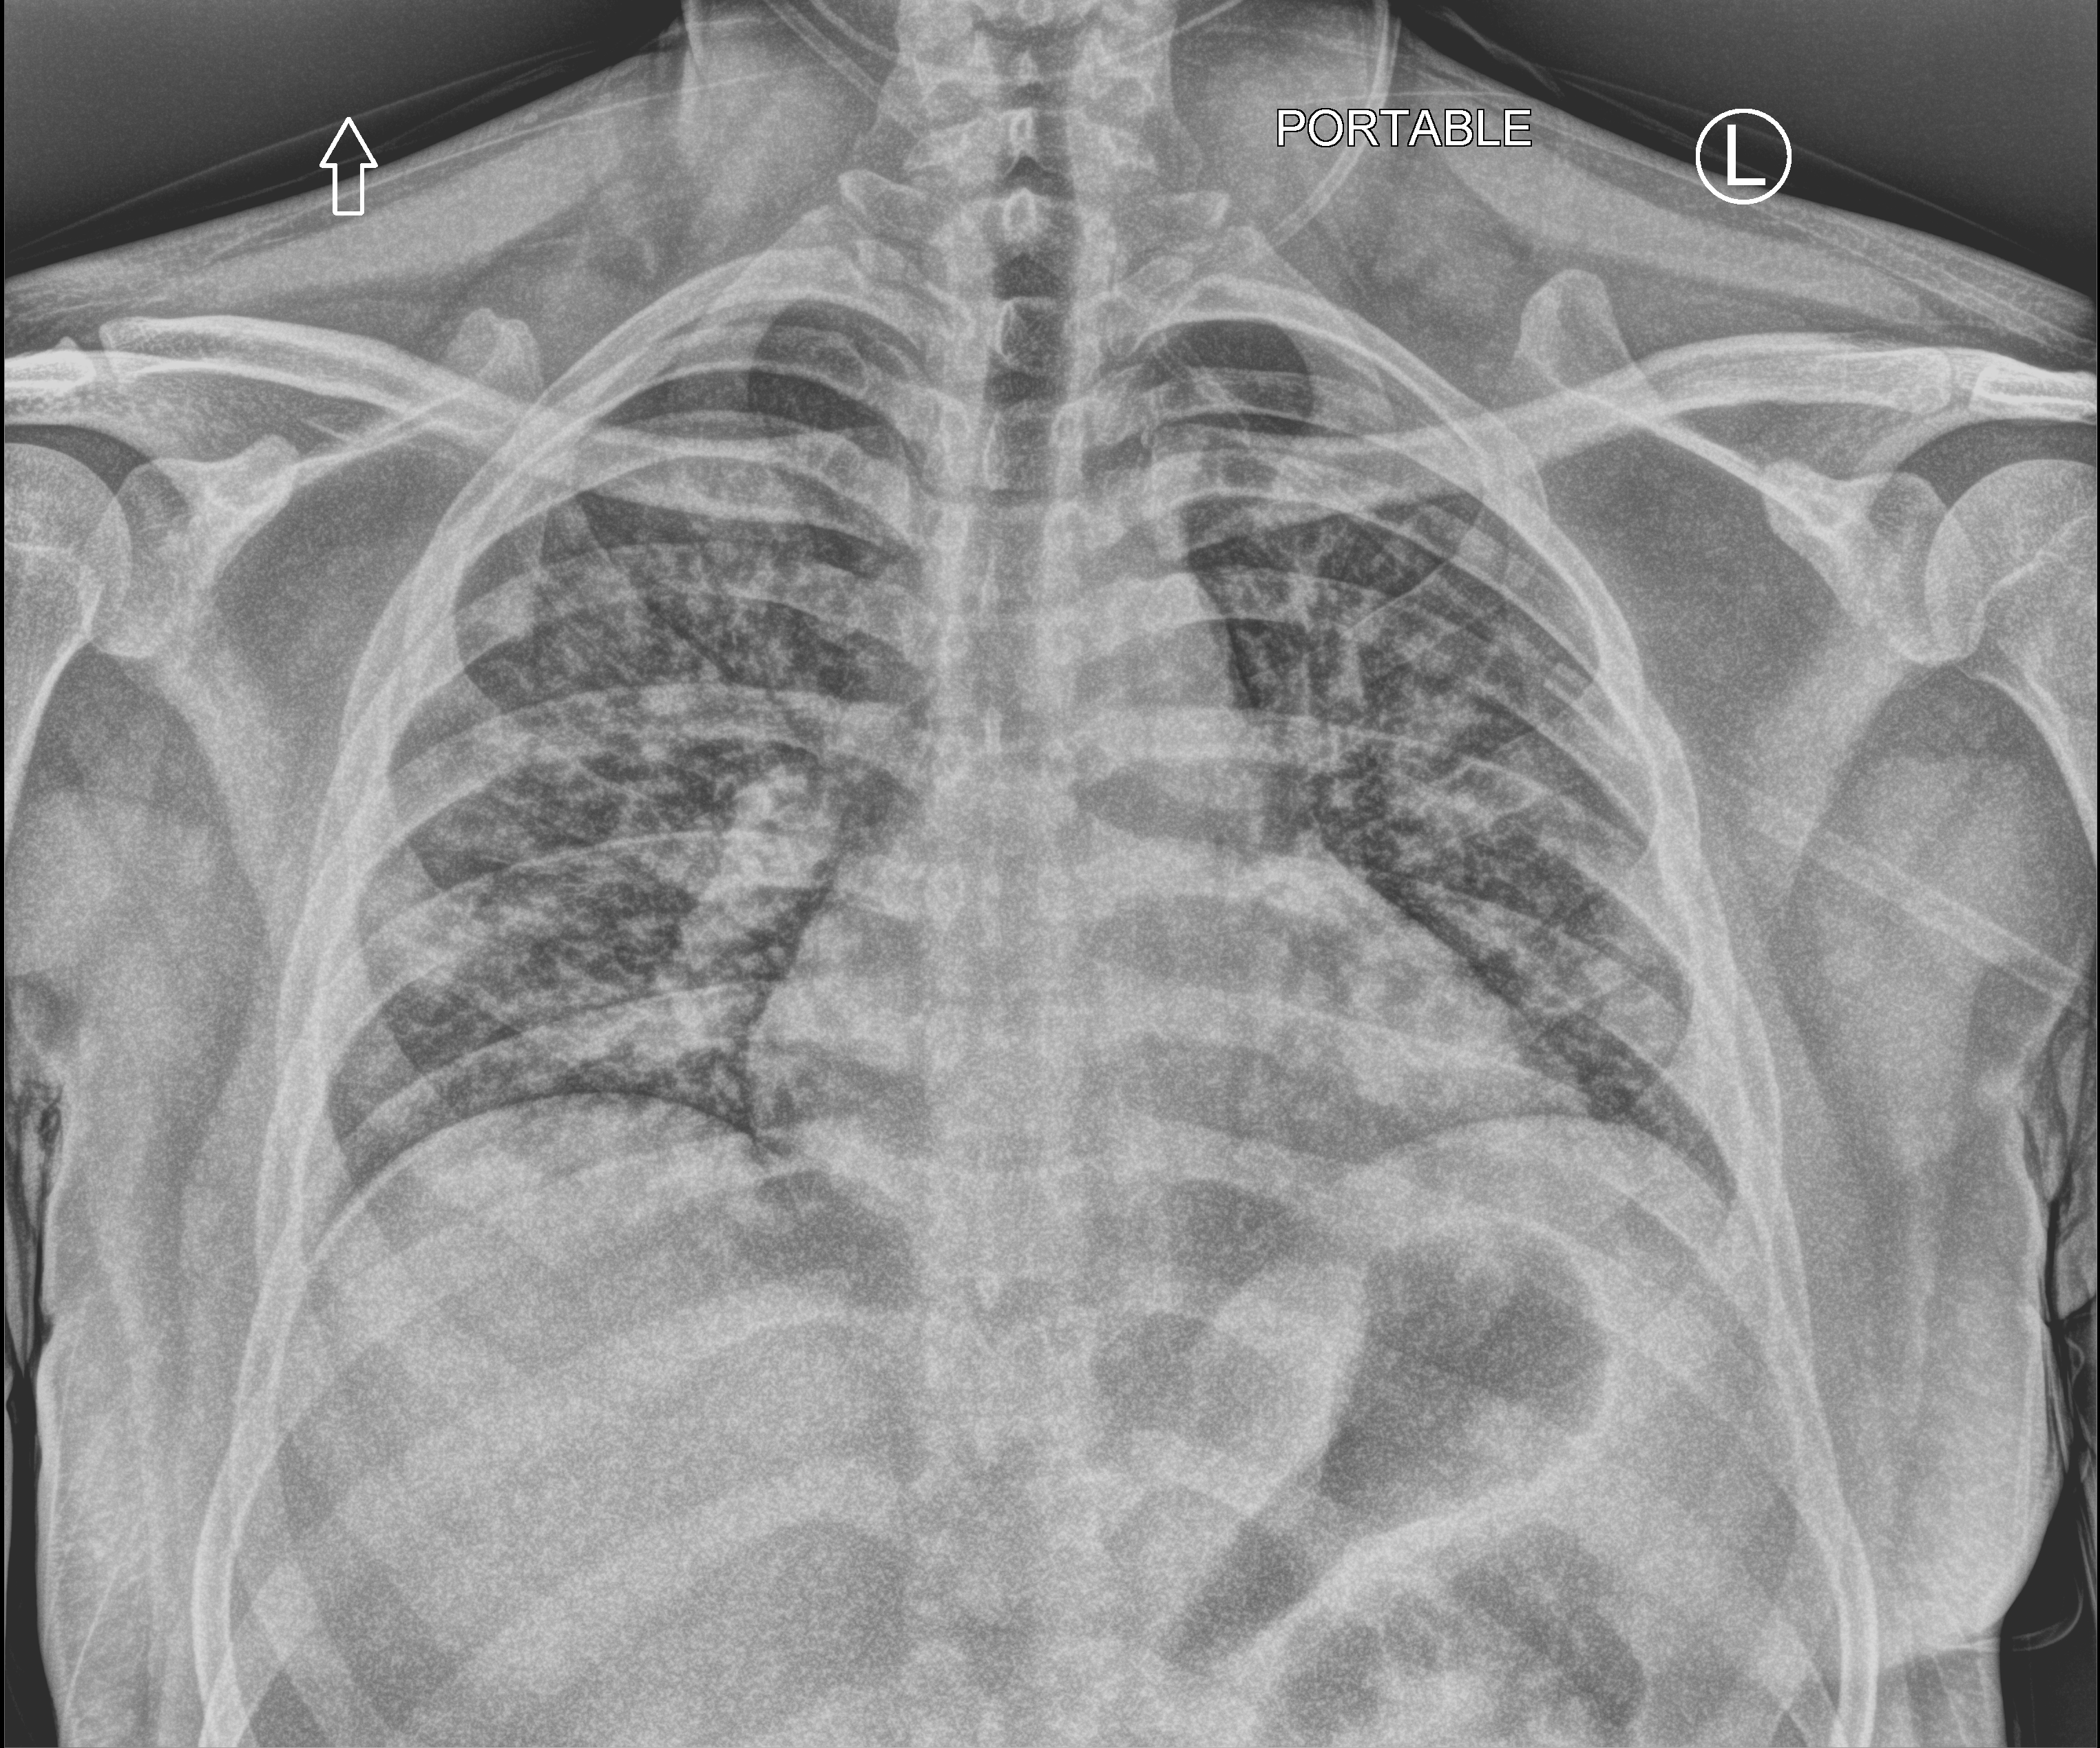
Portable chest radiograph; anteroposterior (AP) projection. Male patient hospitalised with COVID-19, age 18–59 years.
Admission-level facts for this patient (not findings on this image; timing relative to this image not recorded): admitted to intensive care during this hospital stay: no; mechanically ventilated during this hospital stay: yes.